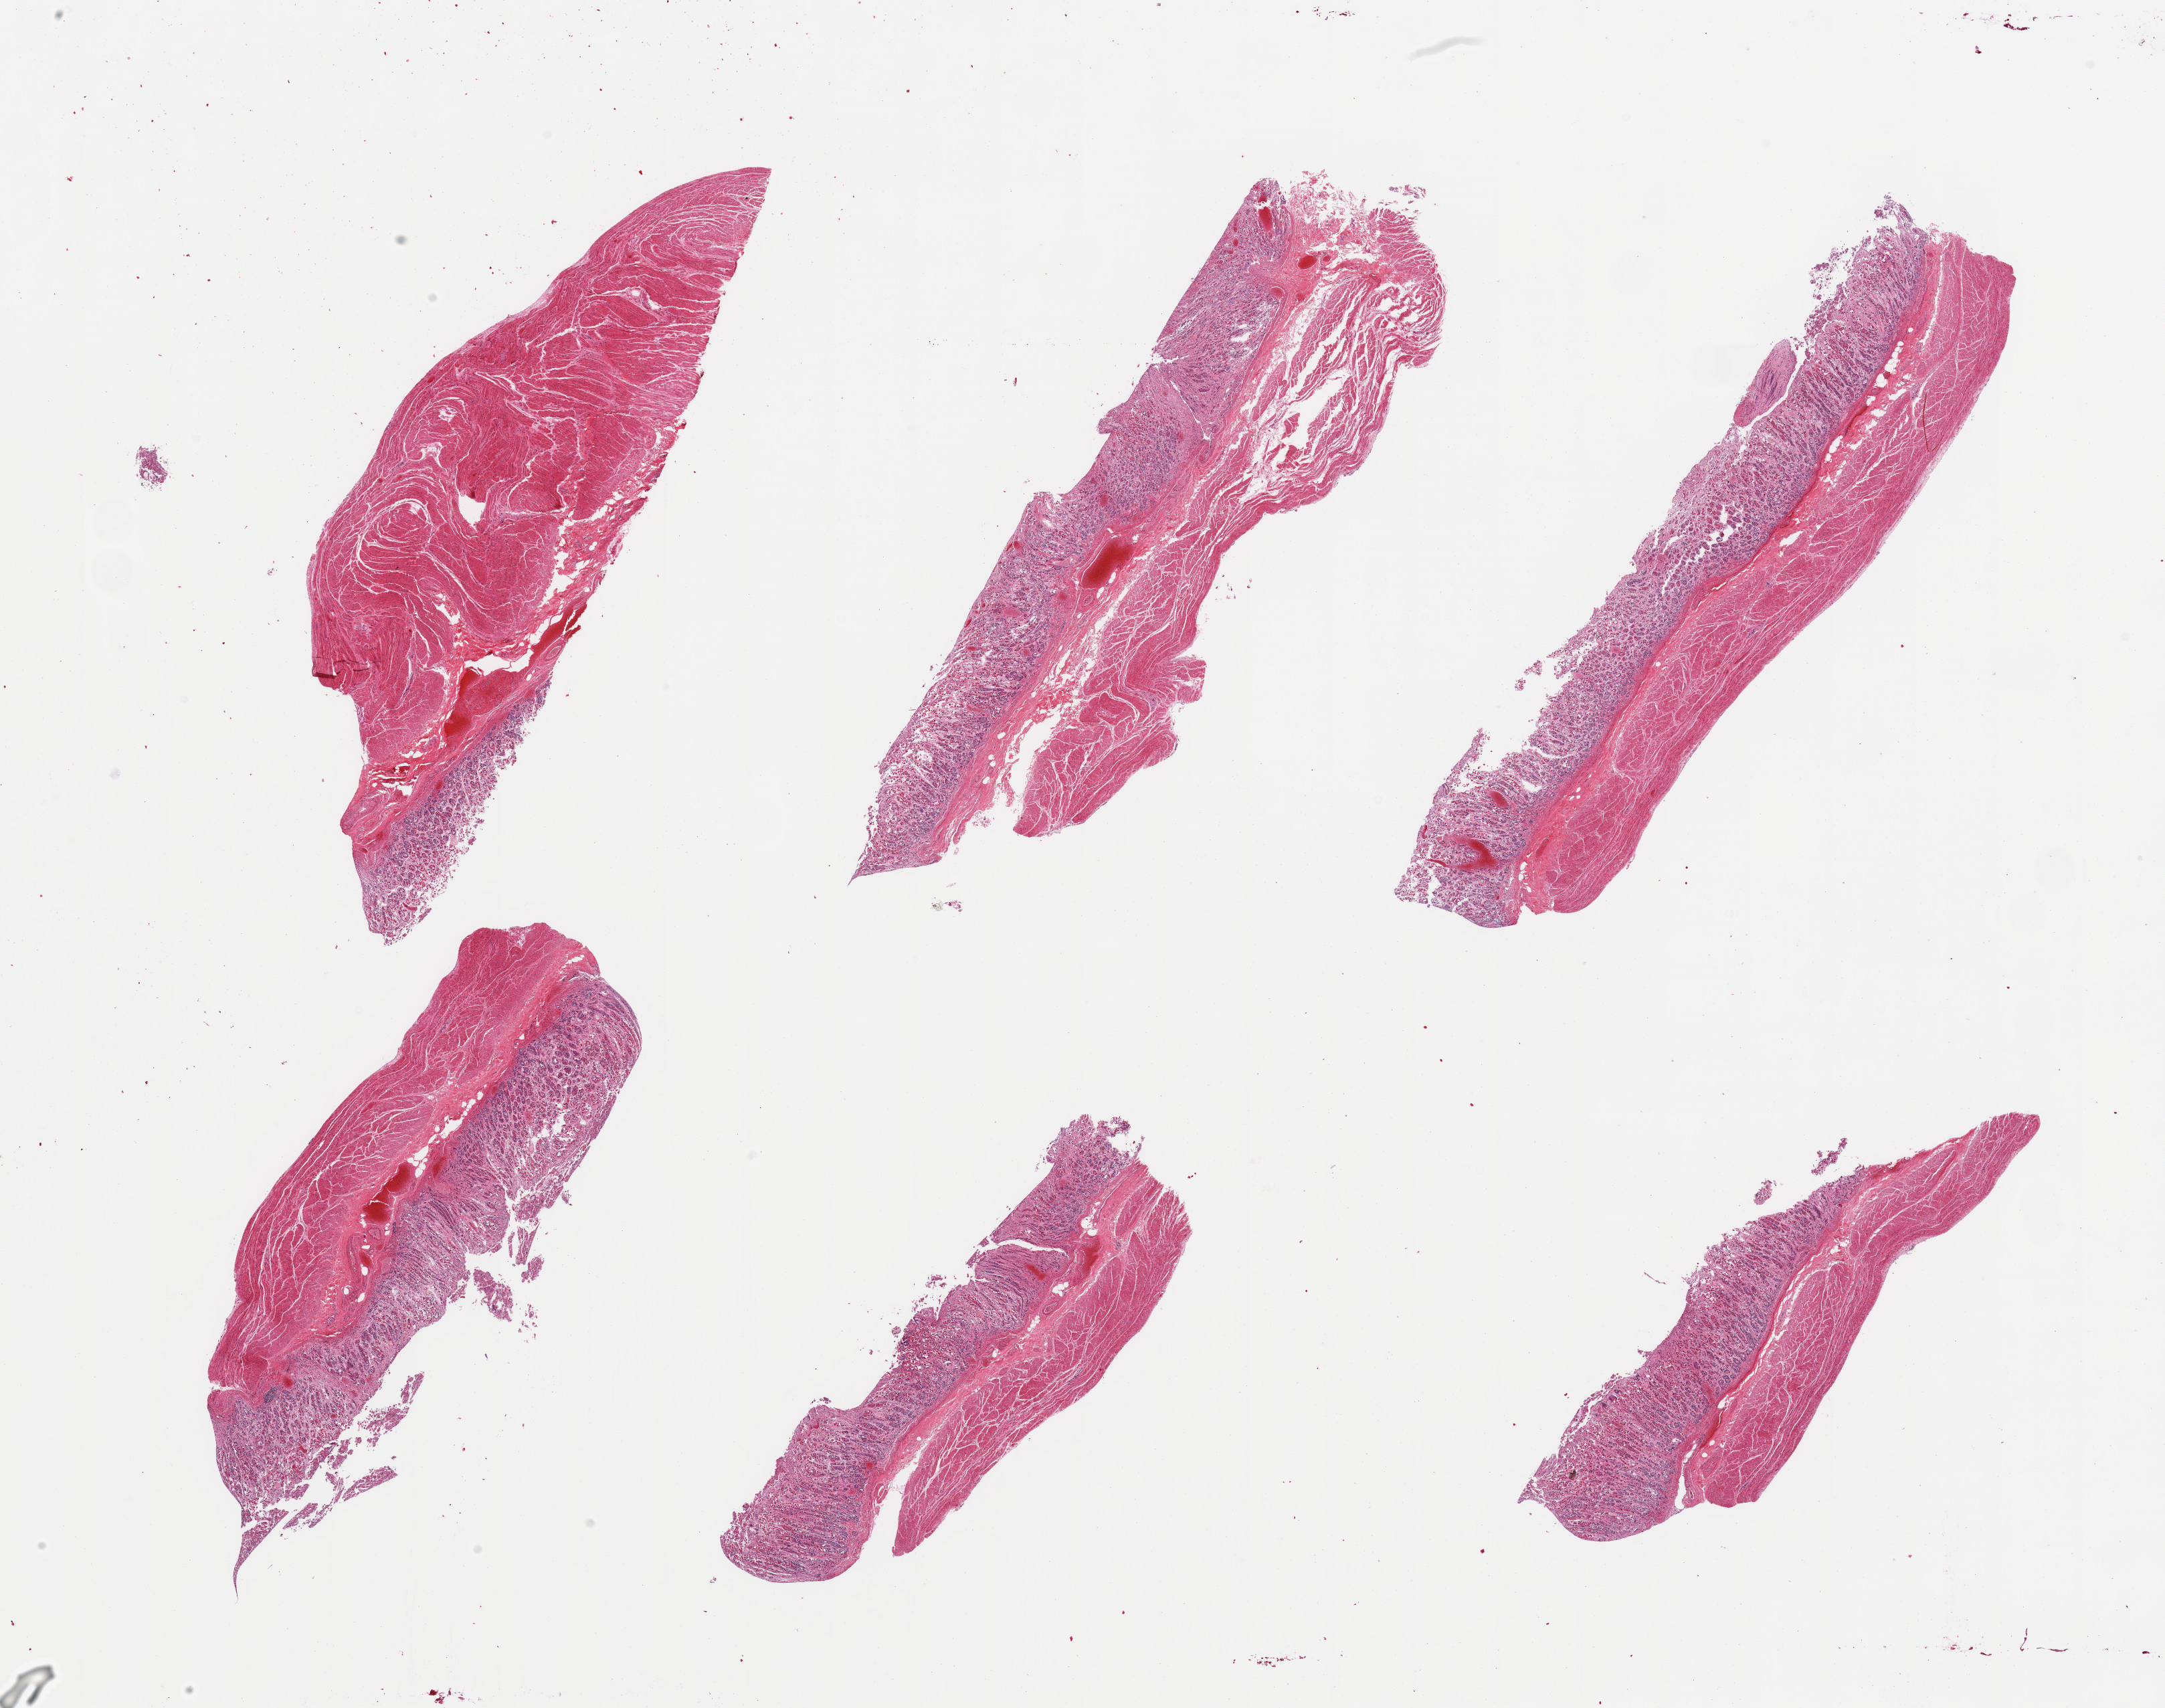
Digitized H&E-stained section, whole scanned area (about 25.6 x 20.2 mm, acquisition: 20x scan) shown as a low-resolution overview; PAXgene-fixed, paraffin-embedded tissue; section of stomach (target tissue); tissue donor sample.
Review note (as recorded): 6 pieces, mucosa up to ~1mm, ~50% of thickness but with moderate-advanced autolysis, partially sloughed.